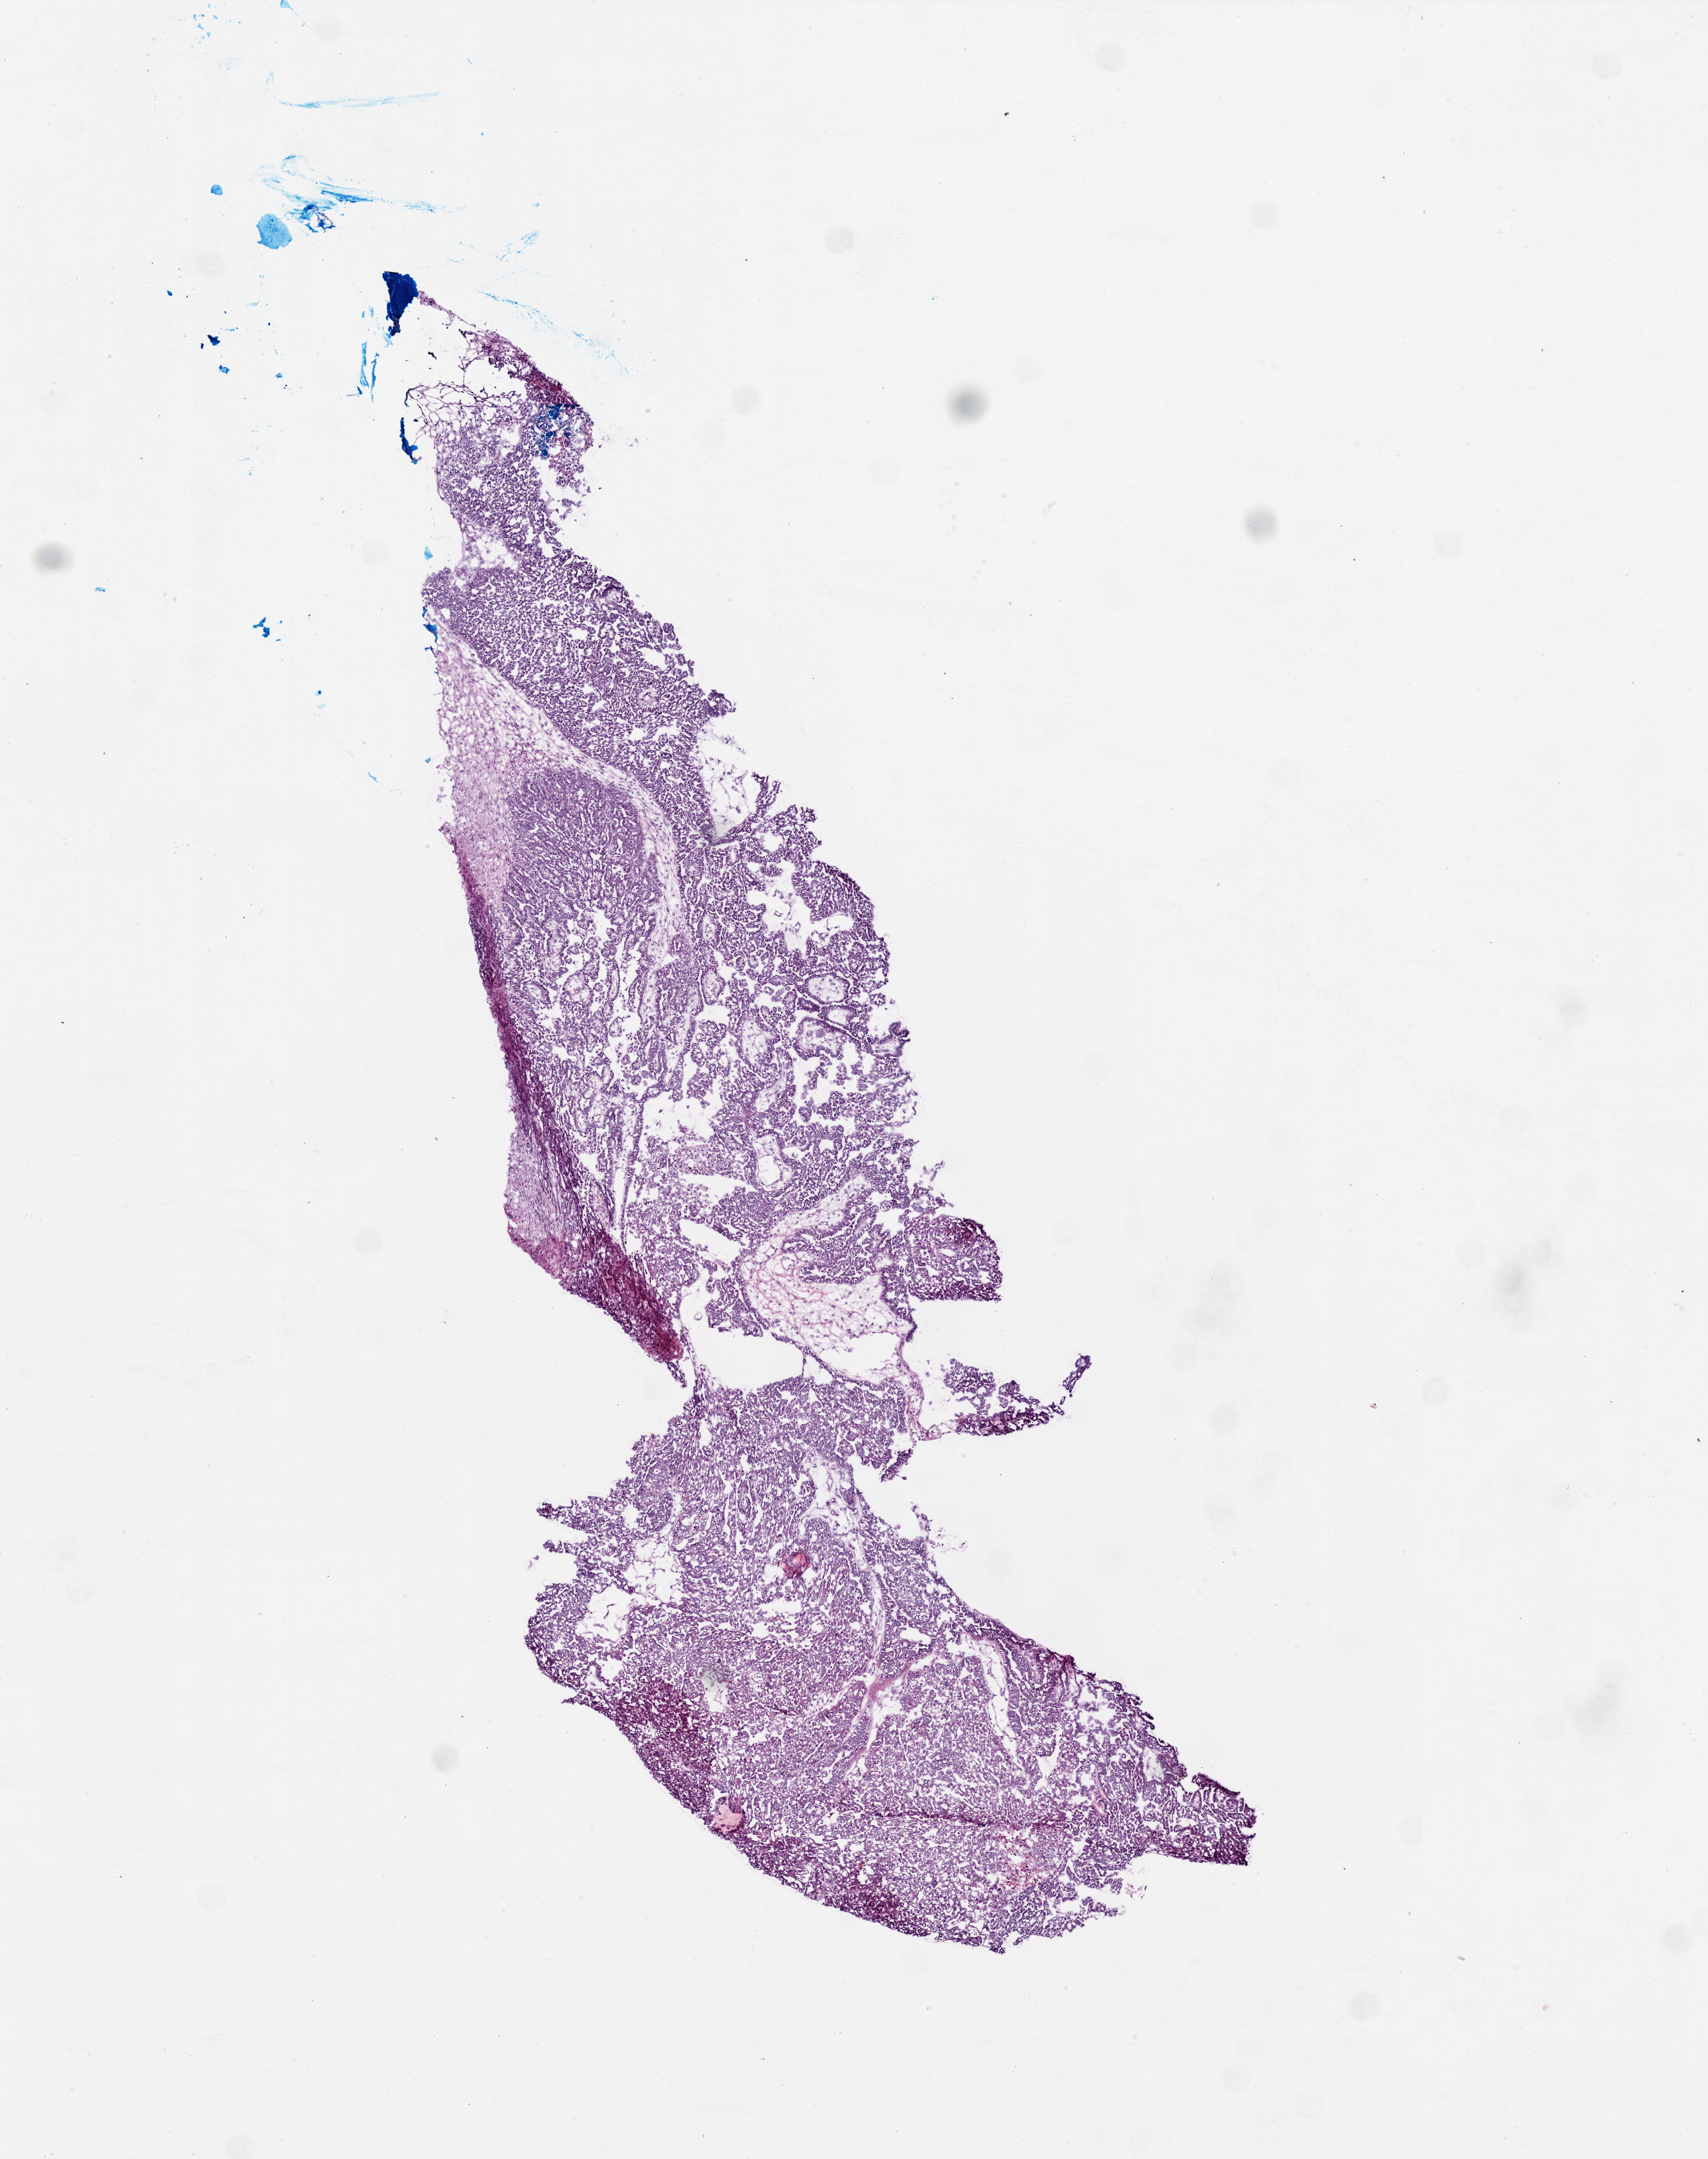
Digitized H&E tissue section (whole slide) — low-resolution overview of the scanned area, about 6.0 x 7.6 mm (acquisition: 20x scan). Frozen section from the top of the tissue portion. Ovary, primary tumour sample. Female patient; age at initial diagnosis 67 years. Histologic grade: G3 (poorly differentiated). Pathologist review of this section (percent, as recorded): tumour cells 90%, tumour nuclei 95%, normal cells 1%, stromal cells 9%, necrosis 0%.
Diagnosis: Serous cystadenocarcinoma, NOS. FIGO stage: IIIC.